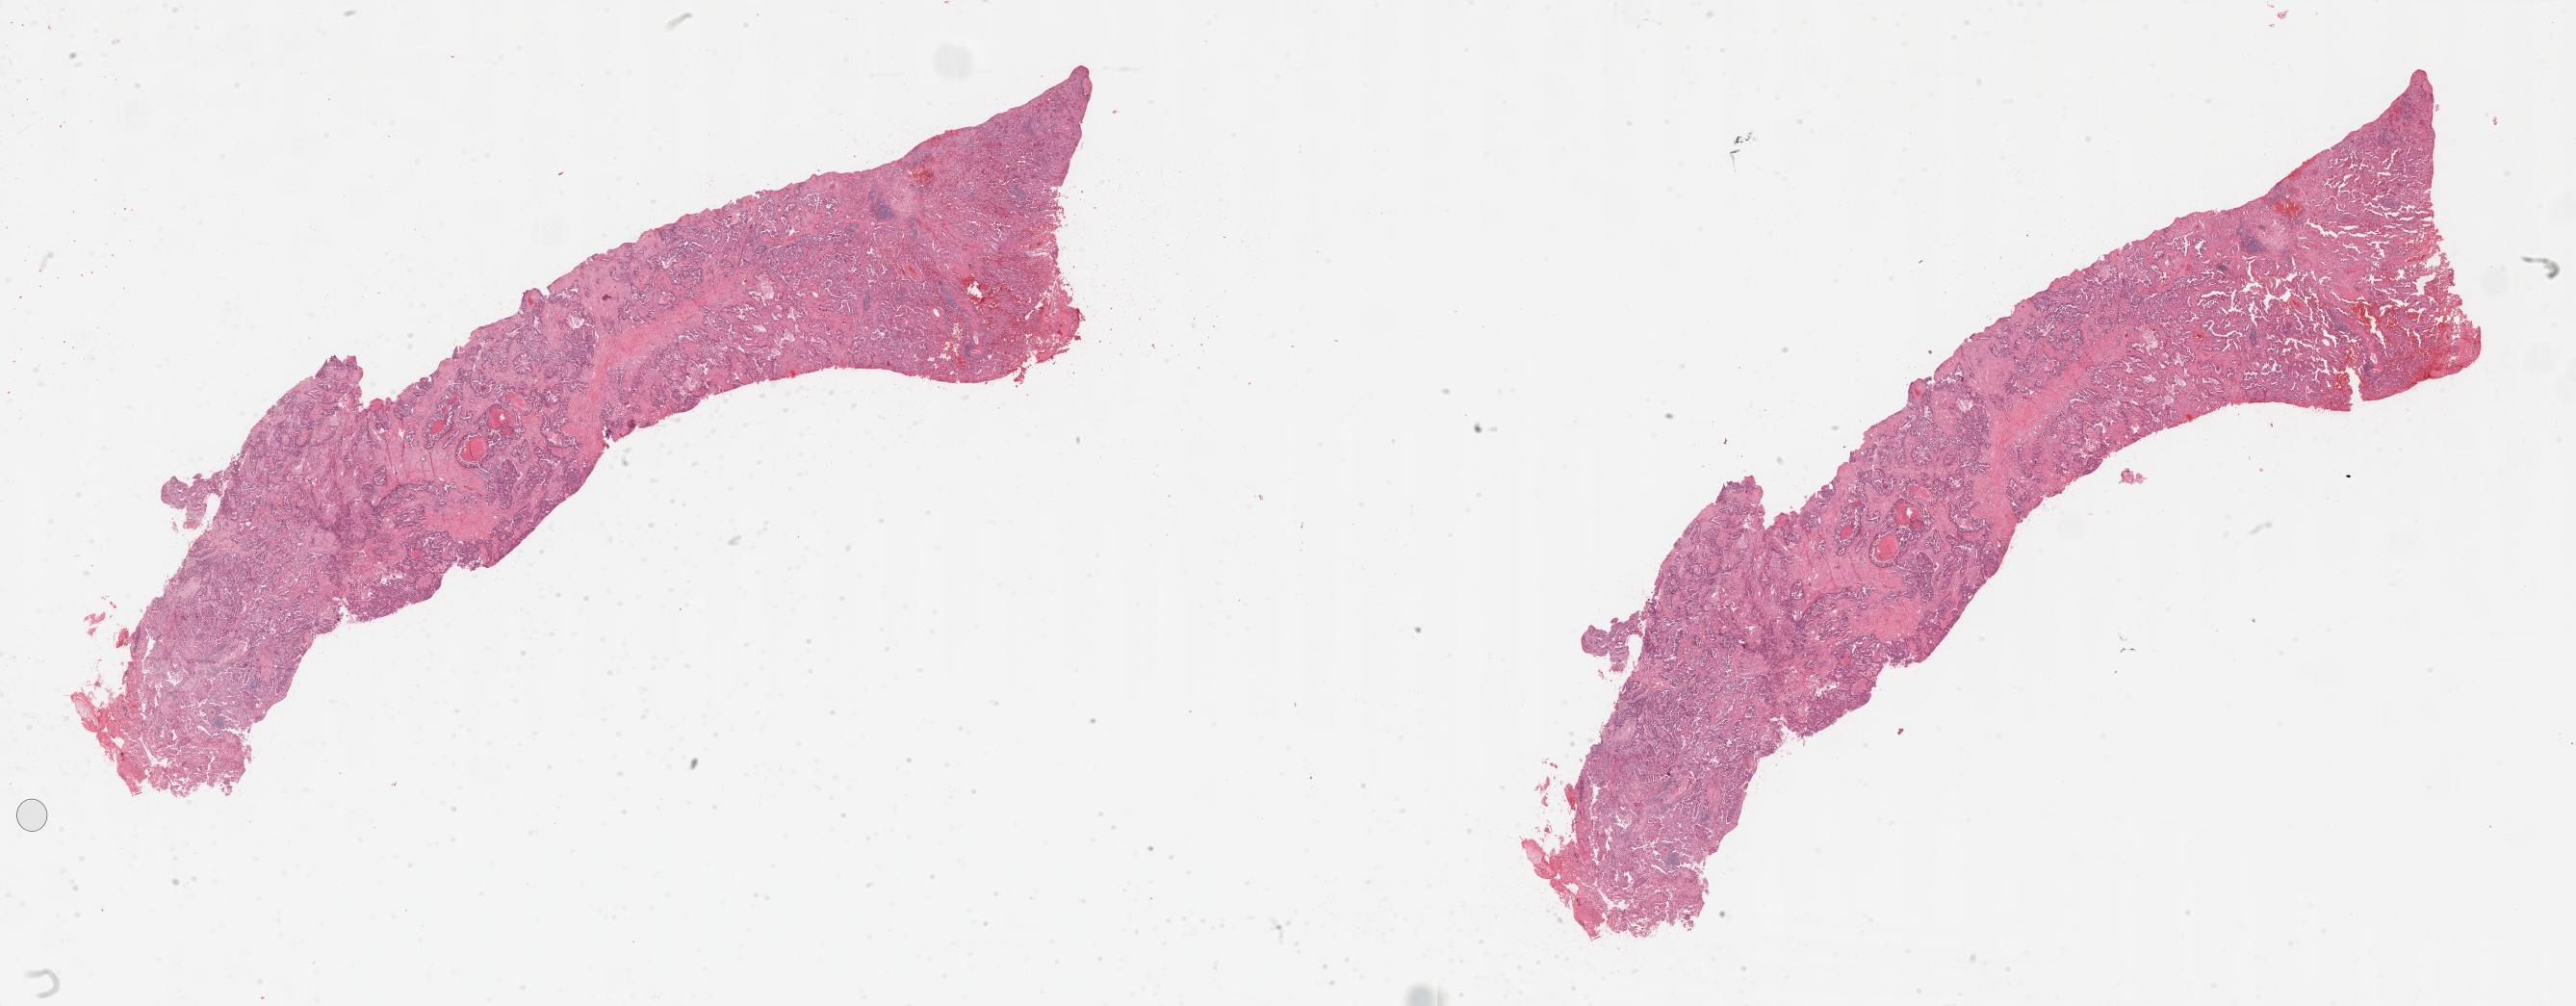
Digitized H&E tissue section (whole slide) — shown as a low-resolution overview of the whole scanned area (about 42.3 x 16.5 mm). Tumour tissue sample, lung. 65-year-old male patient. Histologic grade: G2 (moderately differentiated).
• AJCC pathologic stage: IA
• diagnosis: Adenocarcinoma, NOS
• primary tumour site (as recorded): left upper lobe